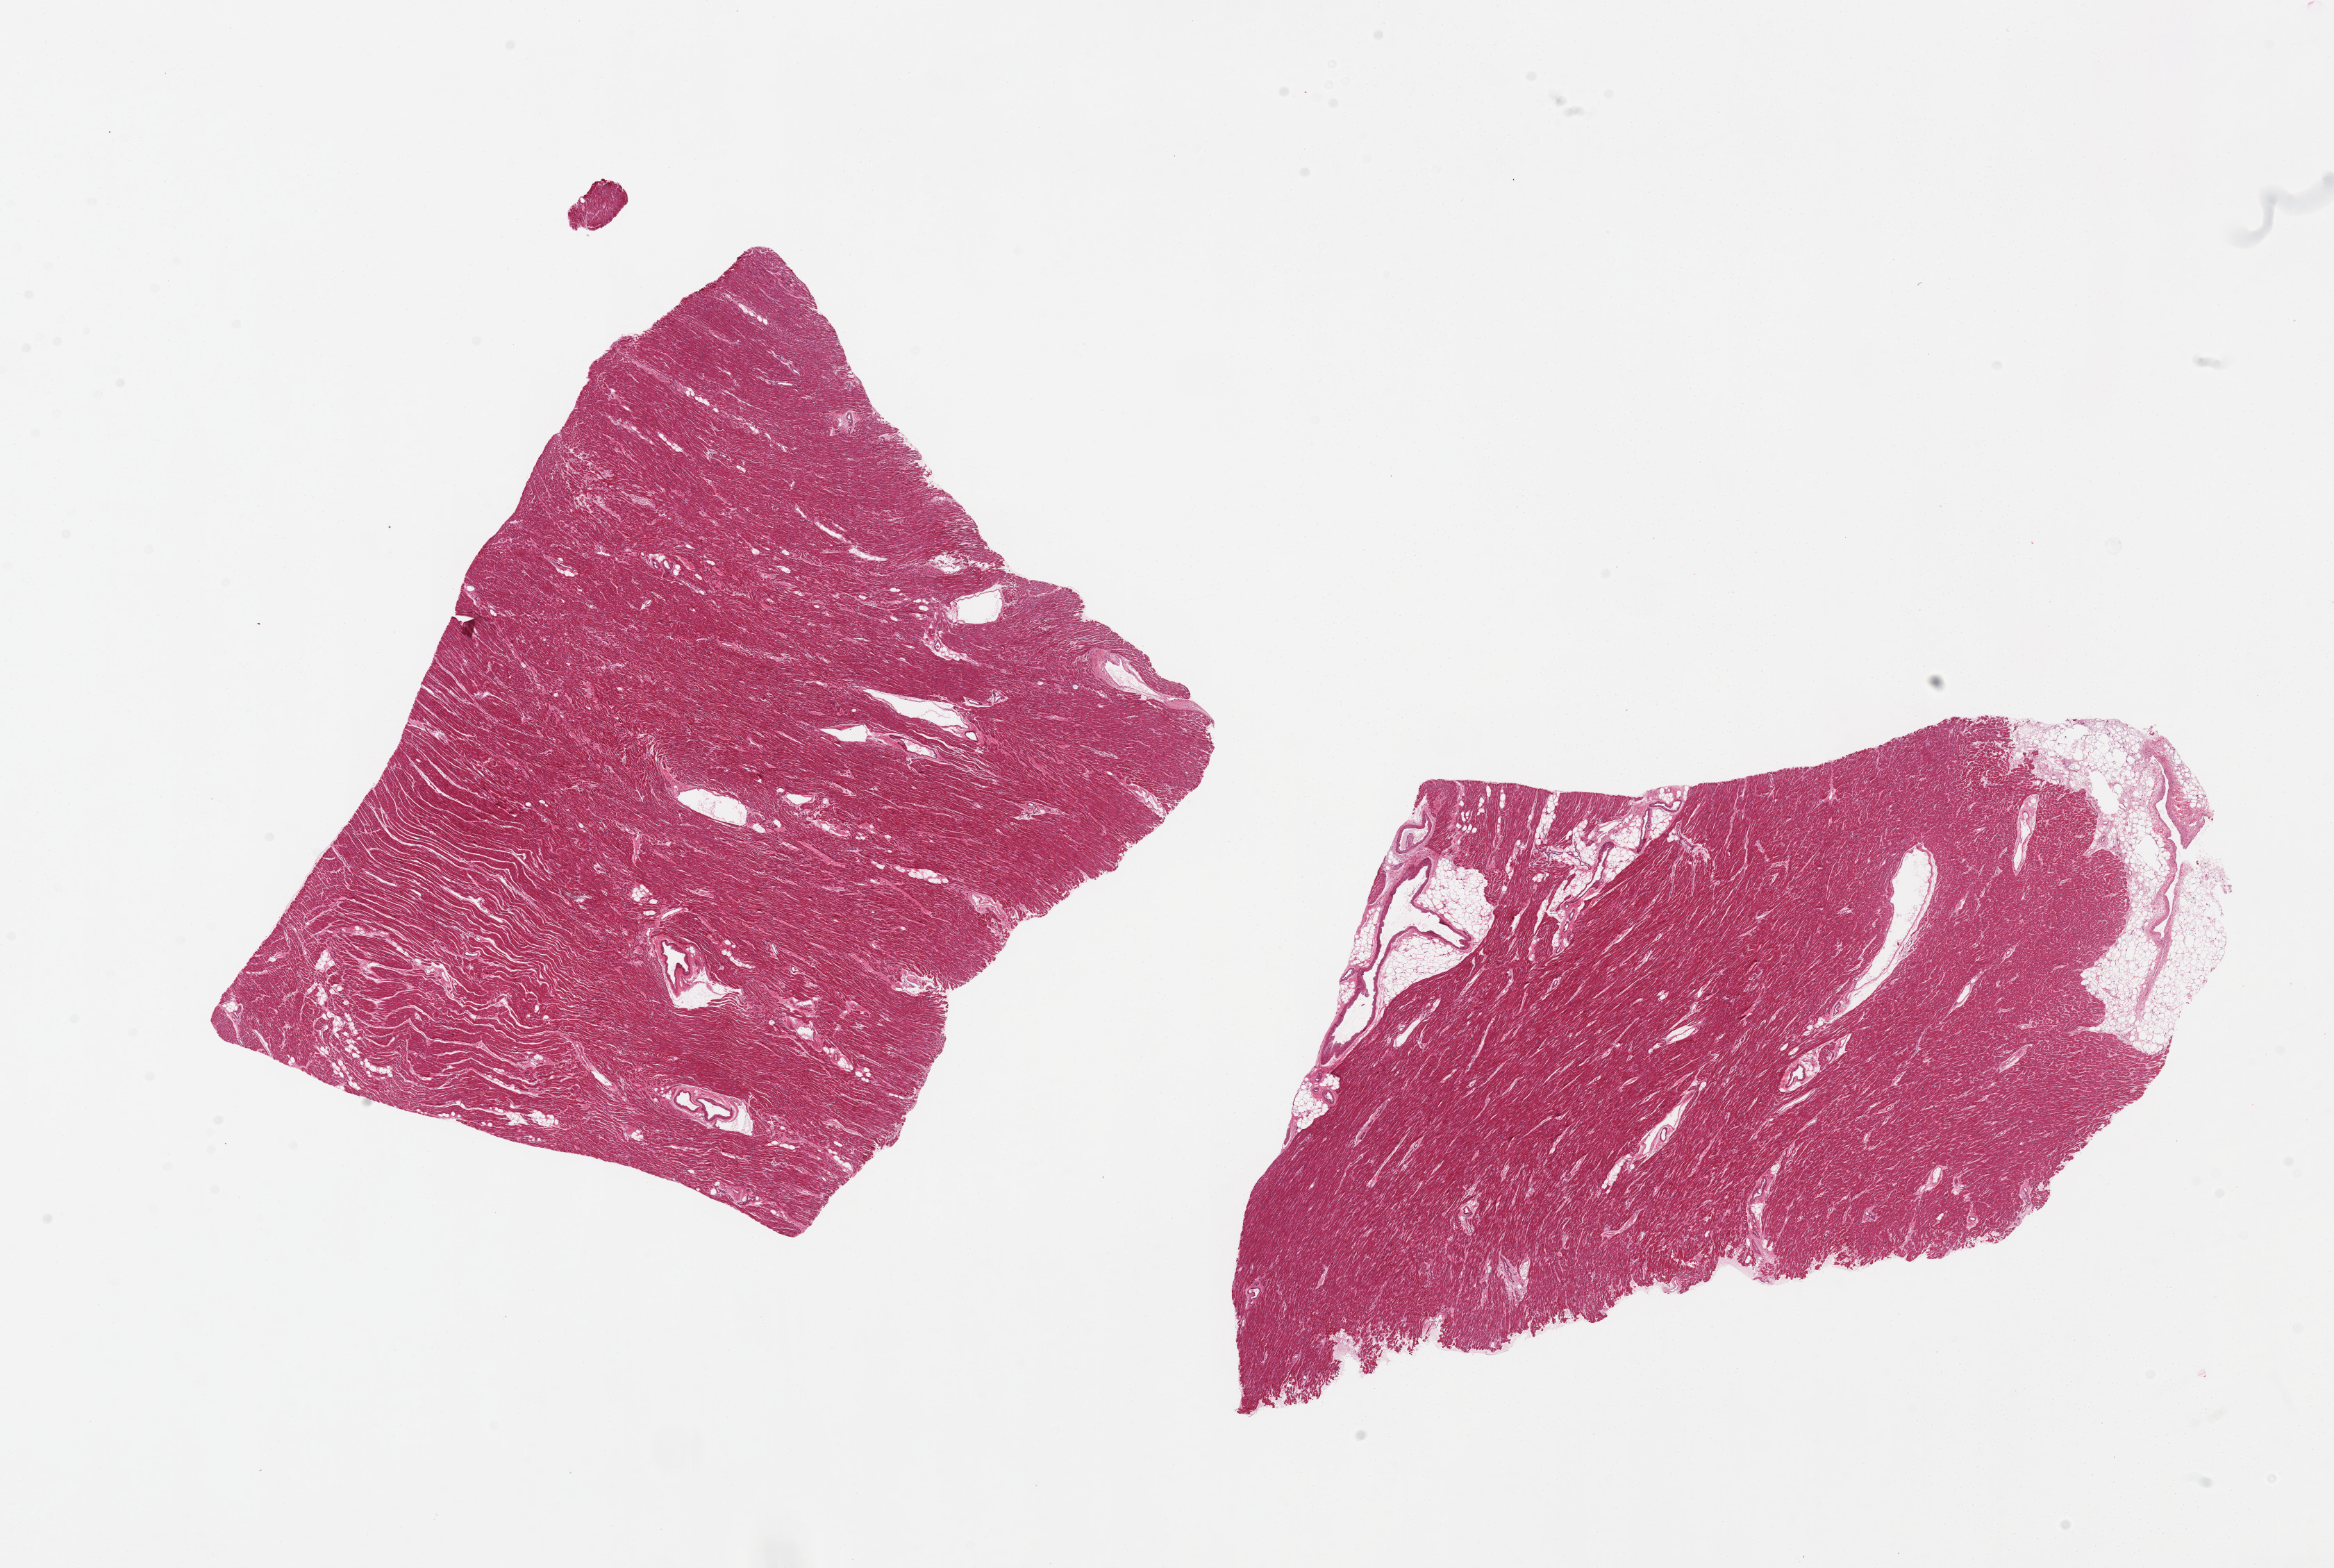
Whole-slide image, H&E stain, brightfield, a low-resolution overview of the entire scanned area, about 26.6 x 17.9 mm; PAXgene-fixed paraffin-embedded (PFPE) section; sampled site (target tissue): heart; tissue donor sample. Donor sex: male.
Reviewer comment on this tissue sample: 2 pieces, one with ~10% adipose tissue.